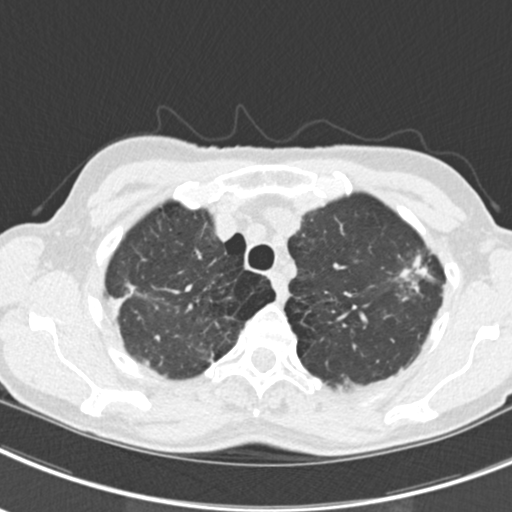
Low-dose screening chest CT, axial slice, second screening round (one year after baseline), lung window (W 1500 / L -600 HU), 2 mm slice thickness, standard (soft-tissue) reconstruction kernel (B30f), slice 42 of 219 in the series, 512 × 512 image matrix. Female, age 63 years at enrolment. Current smoker at enrolment.
Lesion marked by an expert reader, bounding box [x1, y1, x2, y2] px = [382, 241, 448, 303]. The screening reader recorded 9 non-calcified nodules or masses ≥4 mm on this exam (left upper lobe, right upper lobe, left upper lobe, left lower lobe, right middle lobe, left lower lobe, left lower lobe, right lower lobe, right lower lobe); which of them this box marks is not recorded. Official screen result: positive, other.